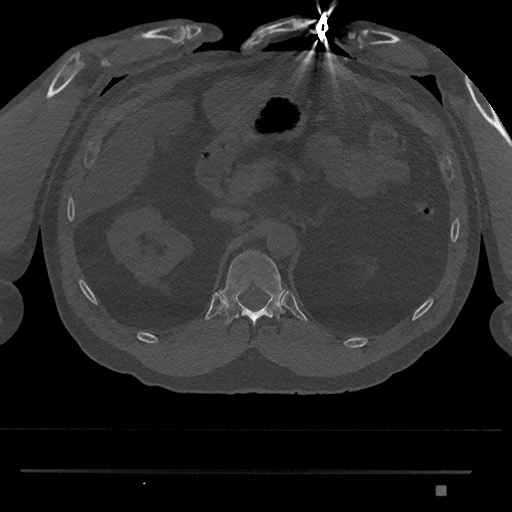
CT including the spine, one axial slice; position 889 of 1134 along the scan axis; reconstruction kernel Br40s/3; 120 kVp; bone window (W 1800 / L 400 HU); 512 × 512 image matrix, field of view 429 × 429 mm. Male patient, age 65 years. From the clinical record (not read from this slice): primary cancer: prostate.
Annotated regions visible in this slice (semi-automatic segmentation, software-assisted and operator-edited):
- T12 vertebra: bounding box <219,250,286,326> (left, top, right, bottom; pixels)